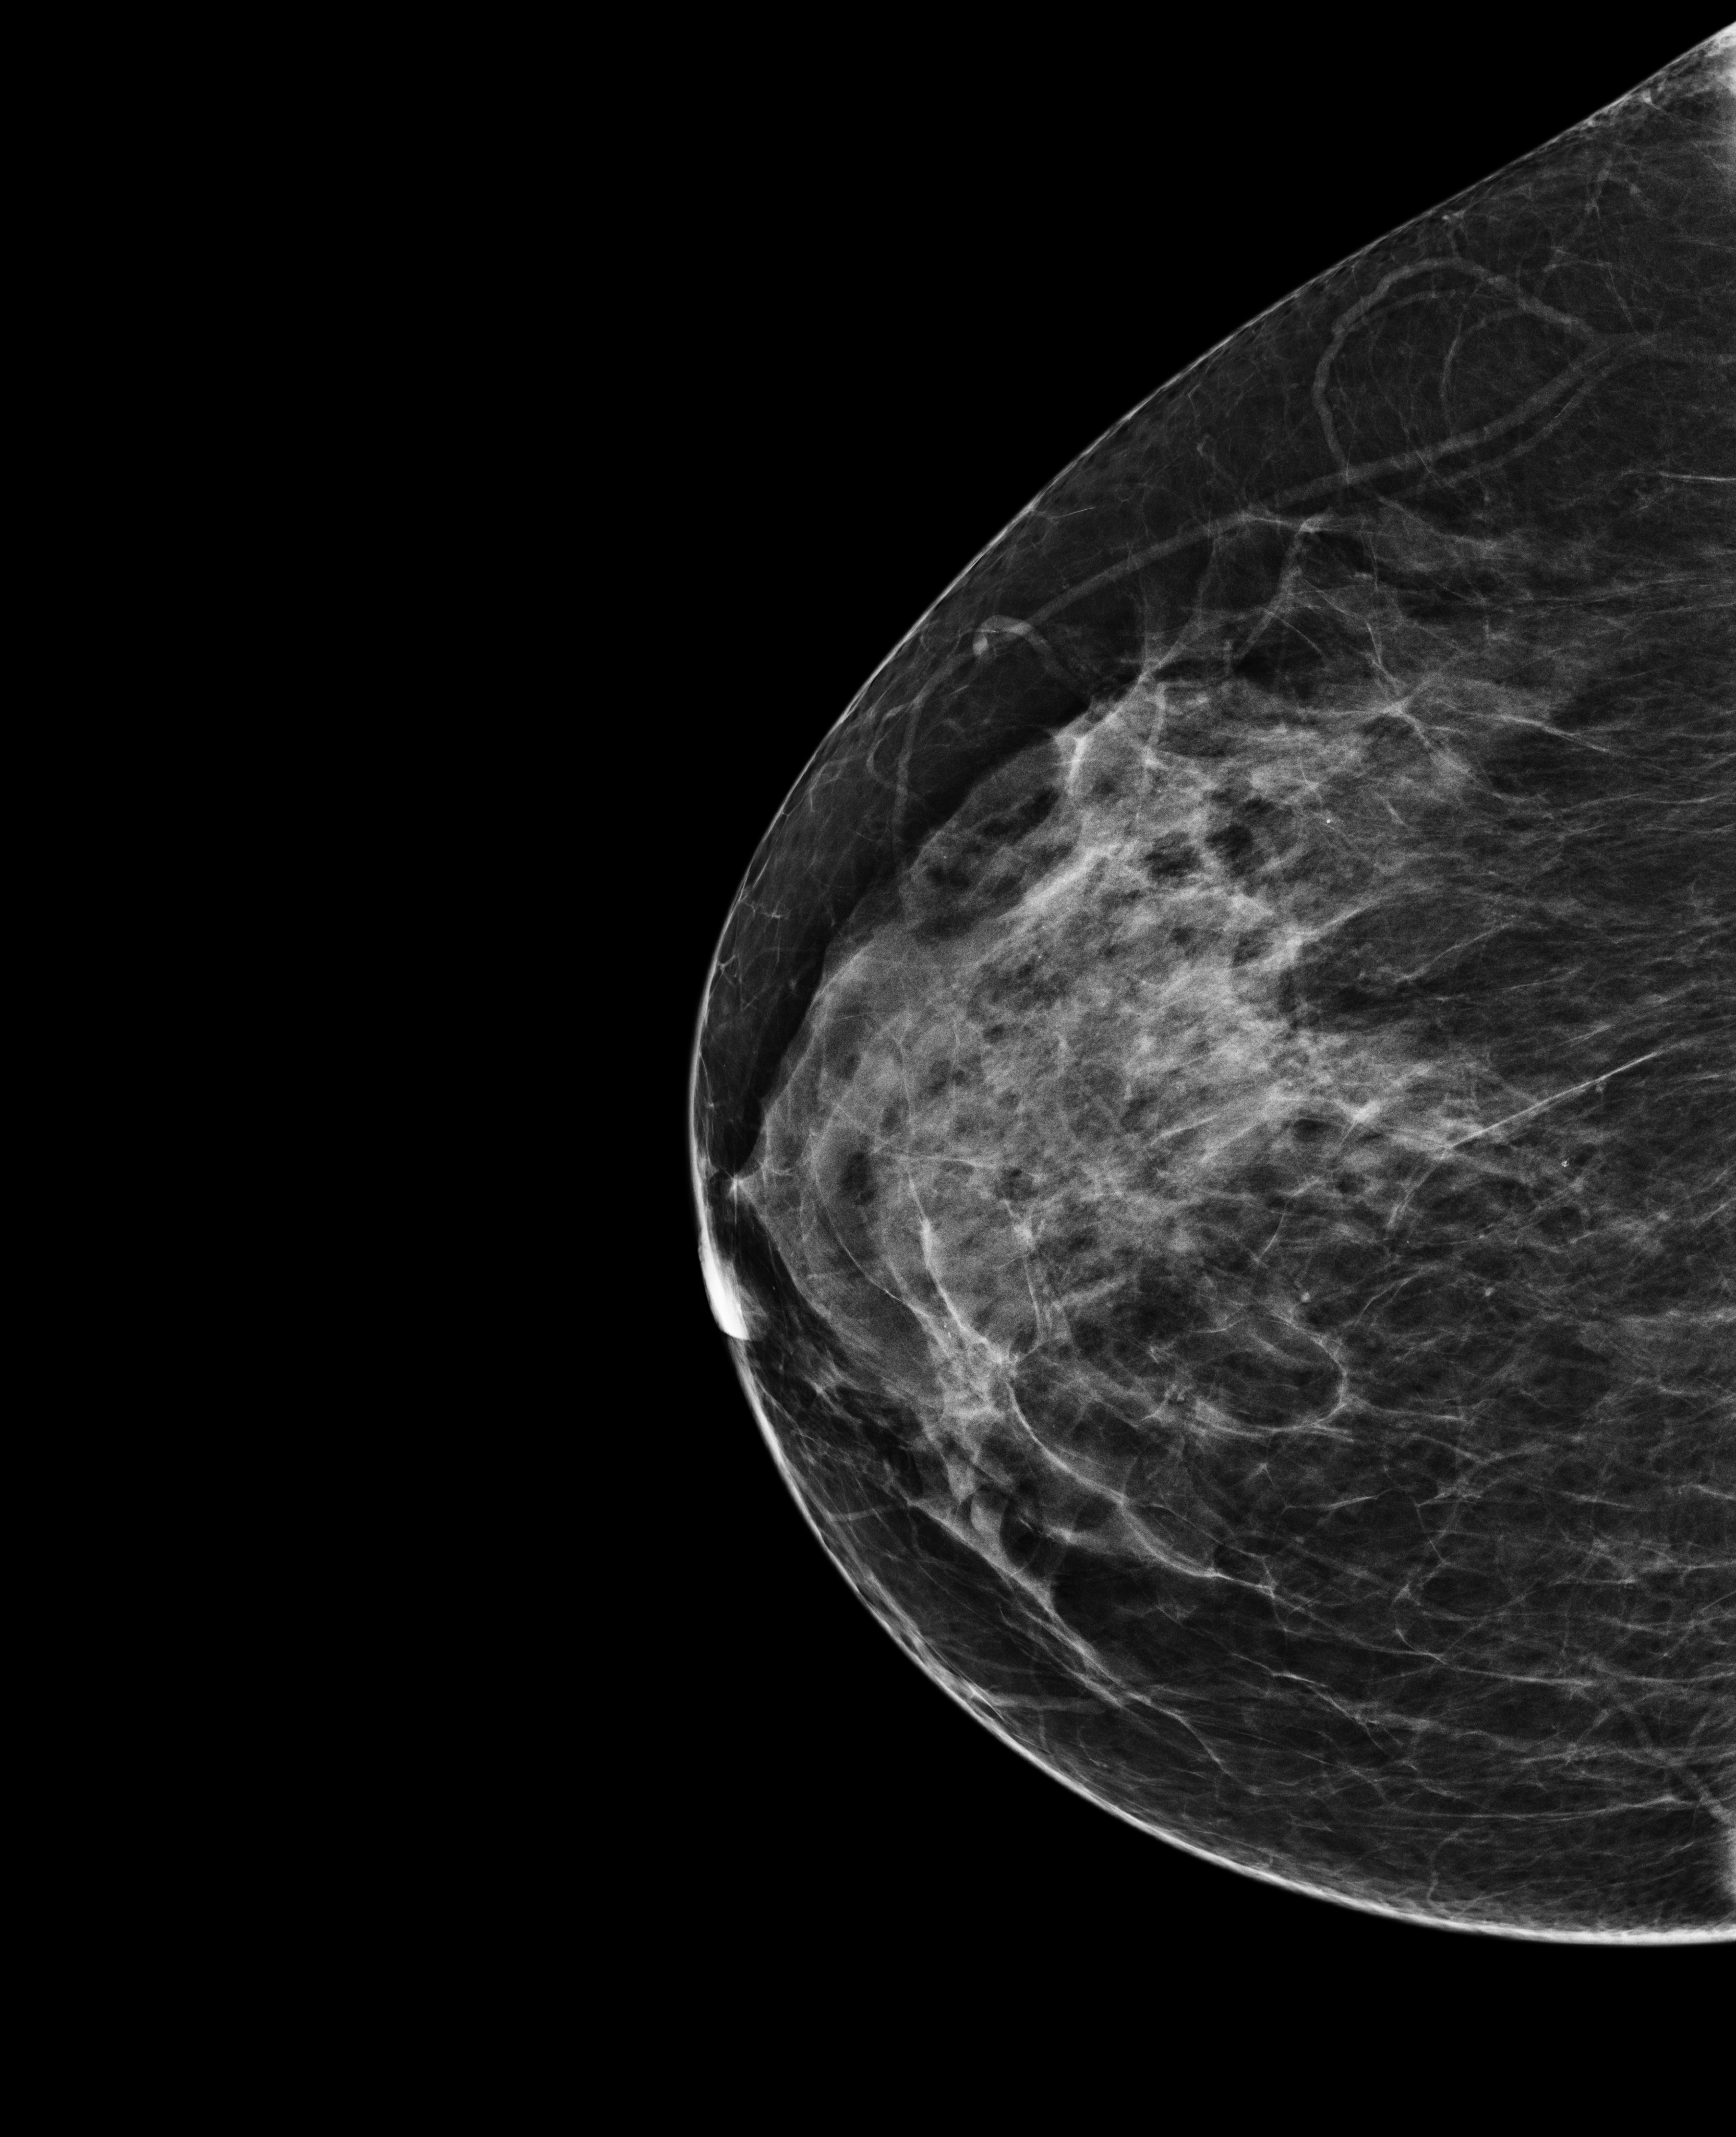
Annual screening mammography examination, compressed breast thickness 65 mm. Patient aged 49 years (female).
Image type: full-field digital mammogram. Breast: right. Projection: craniocaudal (CC) view.